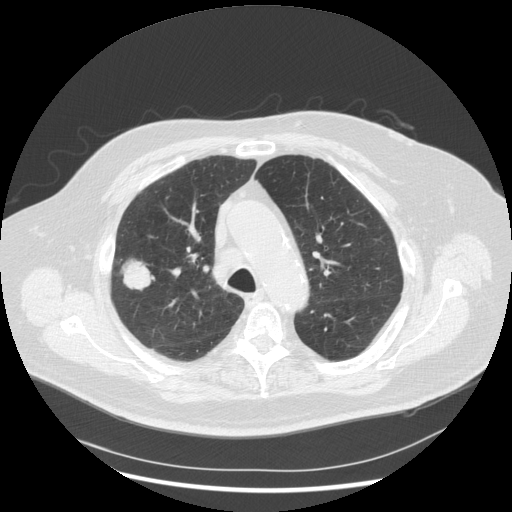
Low-dose screening chest CT, one axial slice. Position 200 of 263 along the scan axis. 120 kVp. Lung window (W 1500 / L -600 HU). 512 × 512 image matrix, field of view 400 × 400 mm.
Annotated regions visible in this slice (manually delineated by an expert):
- lesion 1 (tumor, upper lobe of right lung): bounding box (x1, y1, x2, y2) in pixels: (123, 260, 155, 290)